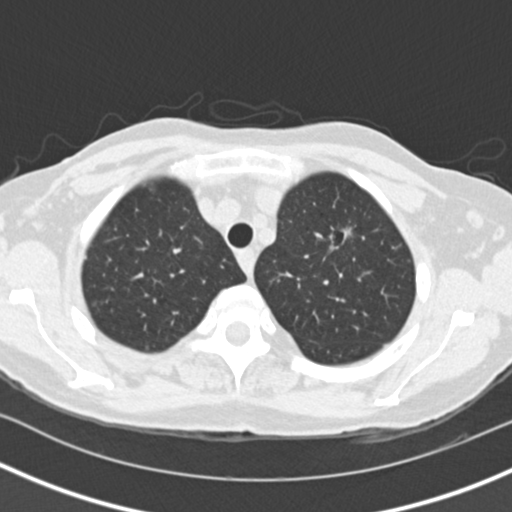
Chest CT (low-dose screening protocol), one axial image, baseline screening round, lung window (W 1500 / L -600 HU). Female, age 73 years at enrolment.
Expert reader's lesion annotation, bounding box (x1, y1, x2, y2) in pixels: (313, 216, 367, 280). Reader record for this screening exam (exam-level; its link to the box is not recorded): non-calcified nodule or mass ≥4 mm, left upper lobe, 27 × 21 mm, spiculated (stellate) margins, soft tissue attenuation. Participant outcome: lung cancer diagnosed 72 days after this screen — bronchiolo-alveolar adenocarcinoma, NOS, left upper lobe, moderately differentiated (G2), stage IIIB (AJCC 6th edition), 17 mm at pathology.